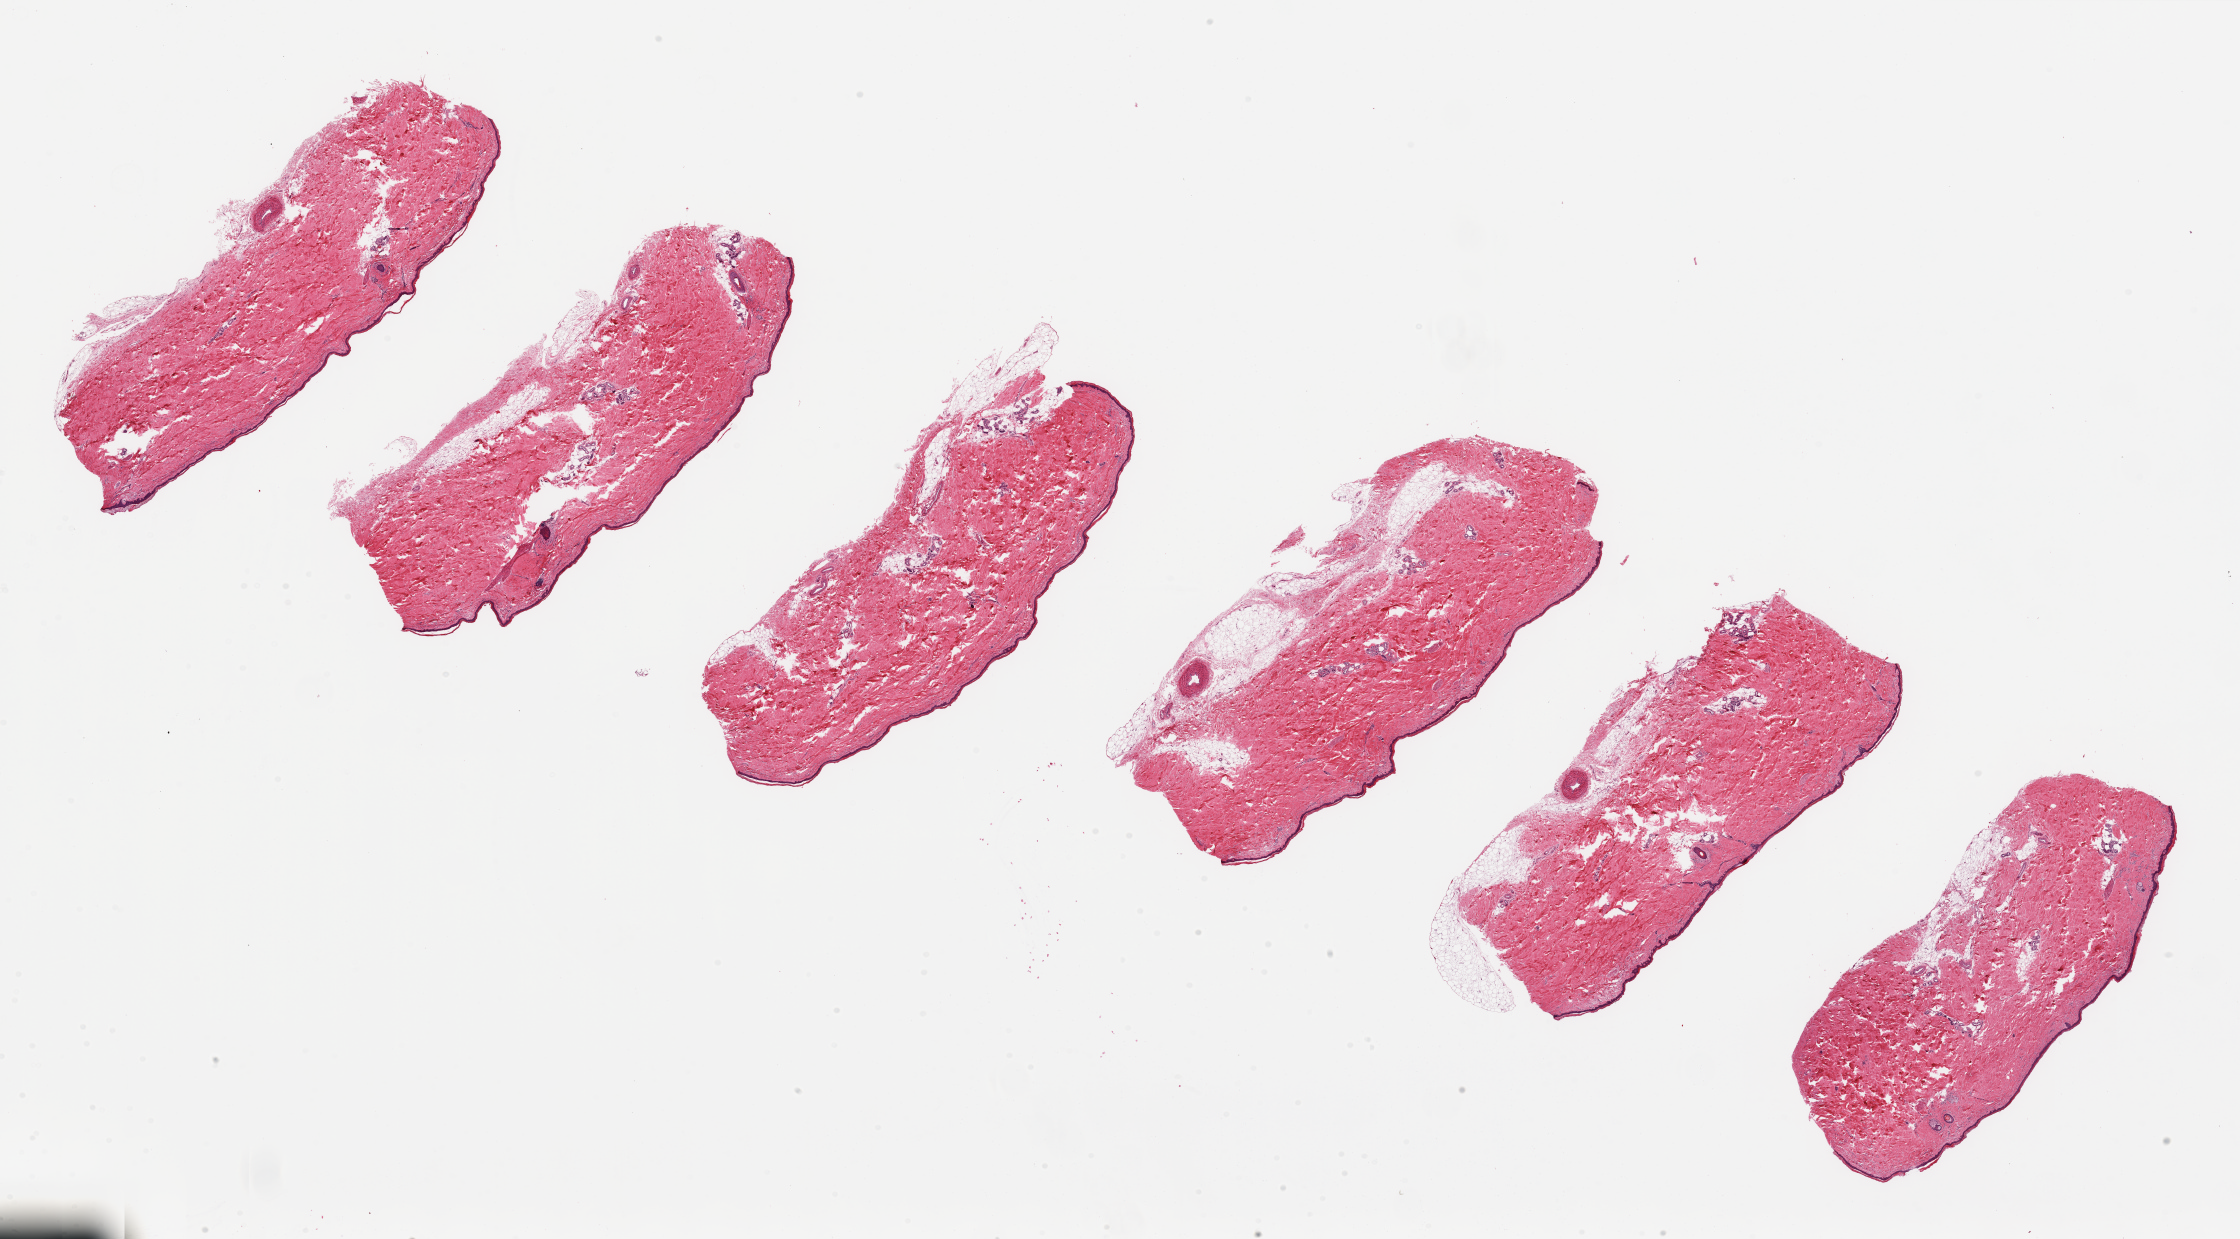
Digitized haematoxylin and eosin-stained section, low-resolution overview of the scanned area, about 35.4 x 19.6 mm (slide scanned at 20x), PAXgene-fixed paraffin-embedded (PFPE) section, sampled site (target tissue): skin of lower leg, donor tissue sample.
Review note (as recorded): 6 ~8x2.5mm pieces. Squamous mucosa is ~1-2% of thickness. Areas of poor fixation with tears.